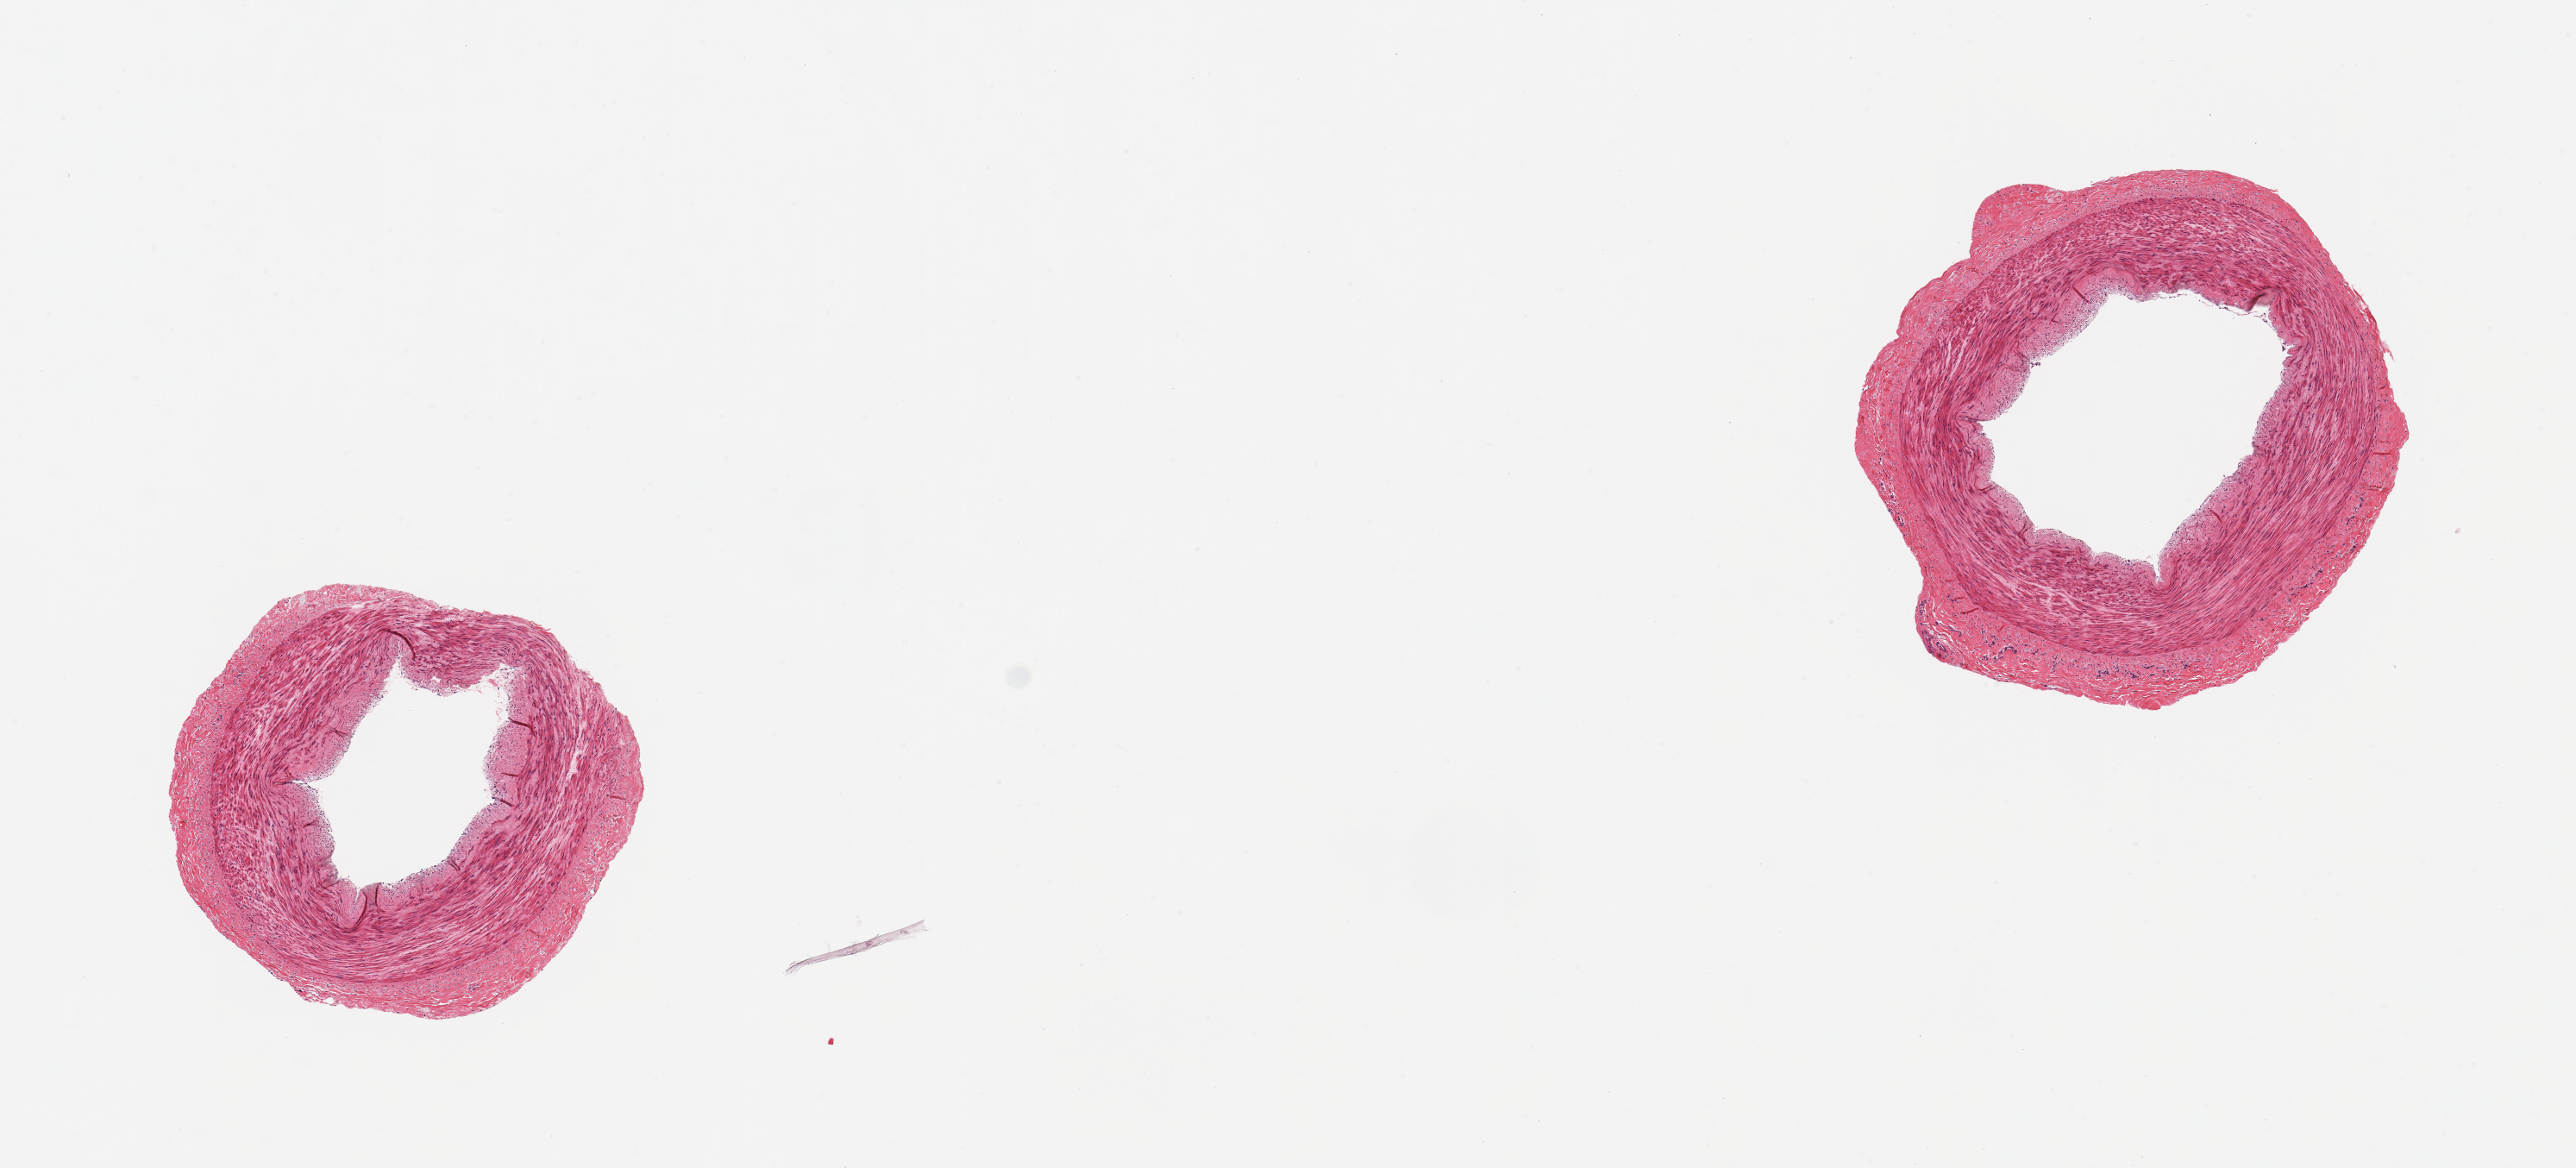
H&E whole-slide image — shown as a low-resolution overview of the whole scanned area (about 11.8 x 5.4 mm, from a 20x scan), PAXgene-fixed paraffin-embedded (PFPE) section, target tissue: tibial artery, tissue donor sample. Donor sex: male.
Pathologist's review note for this sample: 2 pieces; well trimmed; no external fat.